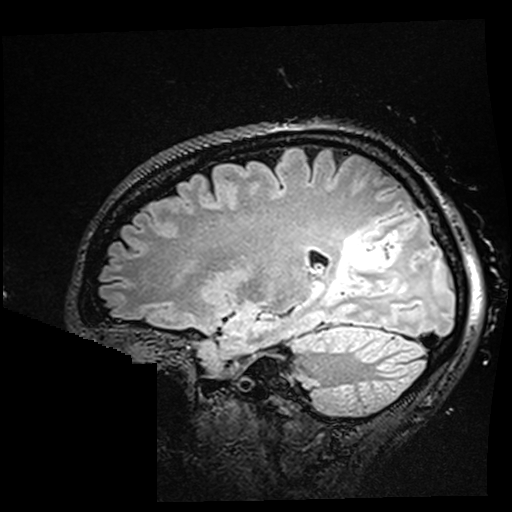
Brain MRI from a brain-tumour surgery series, one sagittal slice; T2 FLAIR; 512 × 512 image matrix. From the clinical record (not read from this slice): histopathology: Oligodendroglioma; WHO grade: 2; IDH mutation: yes; tumour location: Right Parietal.
Outlined on this slice (outlined manually by an expert reader):
- residual tumour: box from (x=329, y=230) to (x=389, y=294) px